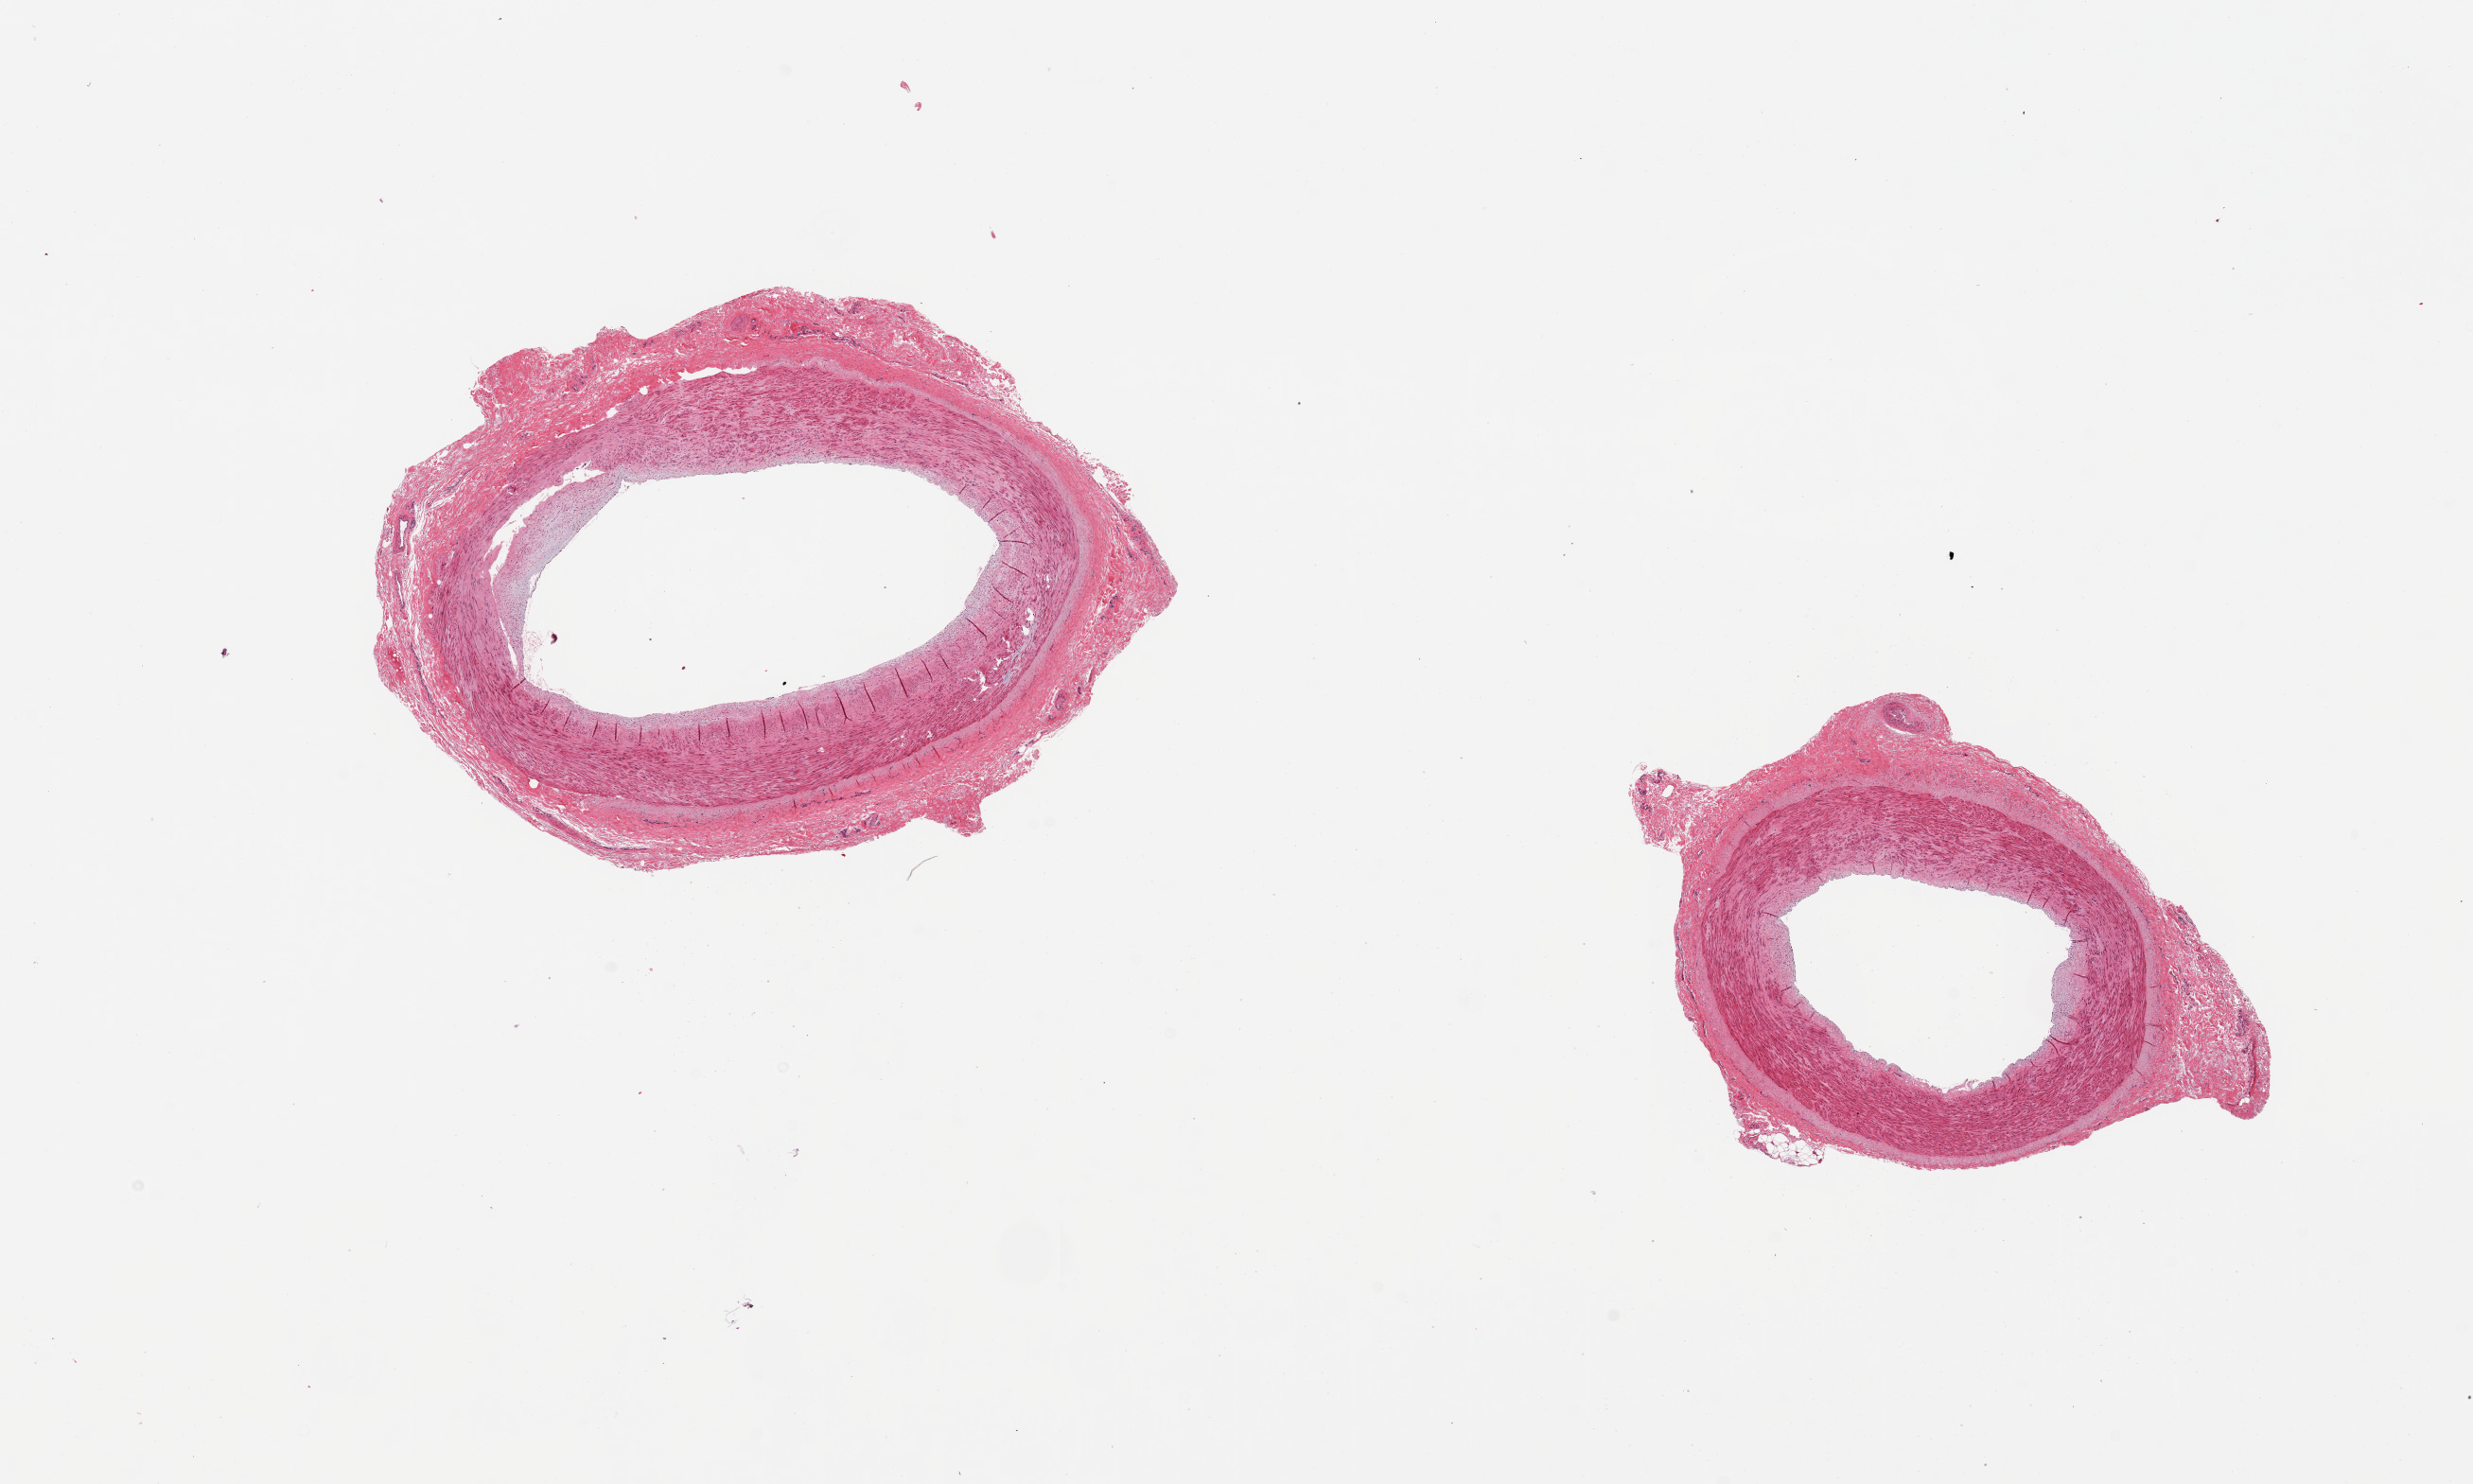
Haematoxylin and eosin whole-slide image — a low-resolution overview of the entire scanned area, about 20.7 x 12.4 mm, PAXgene-fixed paraffin-embedded (PFPE) section, target tissue: tibial artery, tissue donor sample.
Review note (as recorded): 2 pieces. well trimmed.